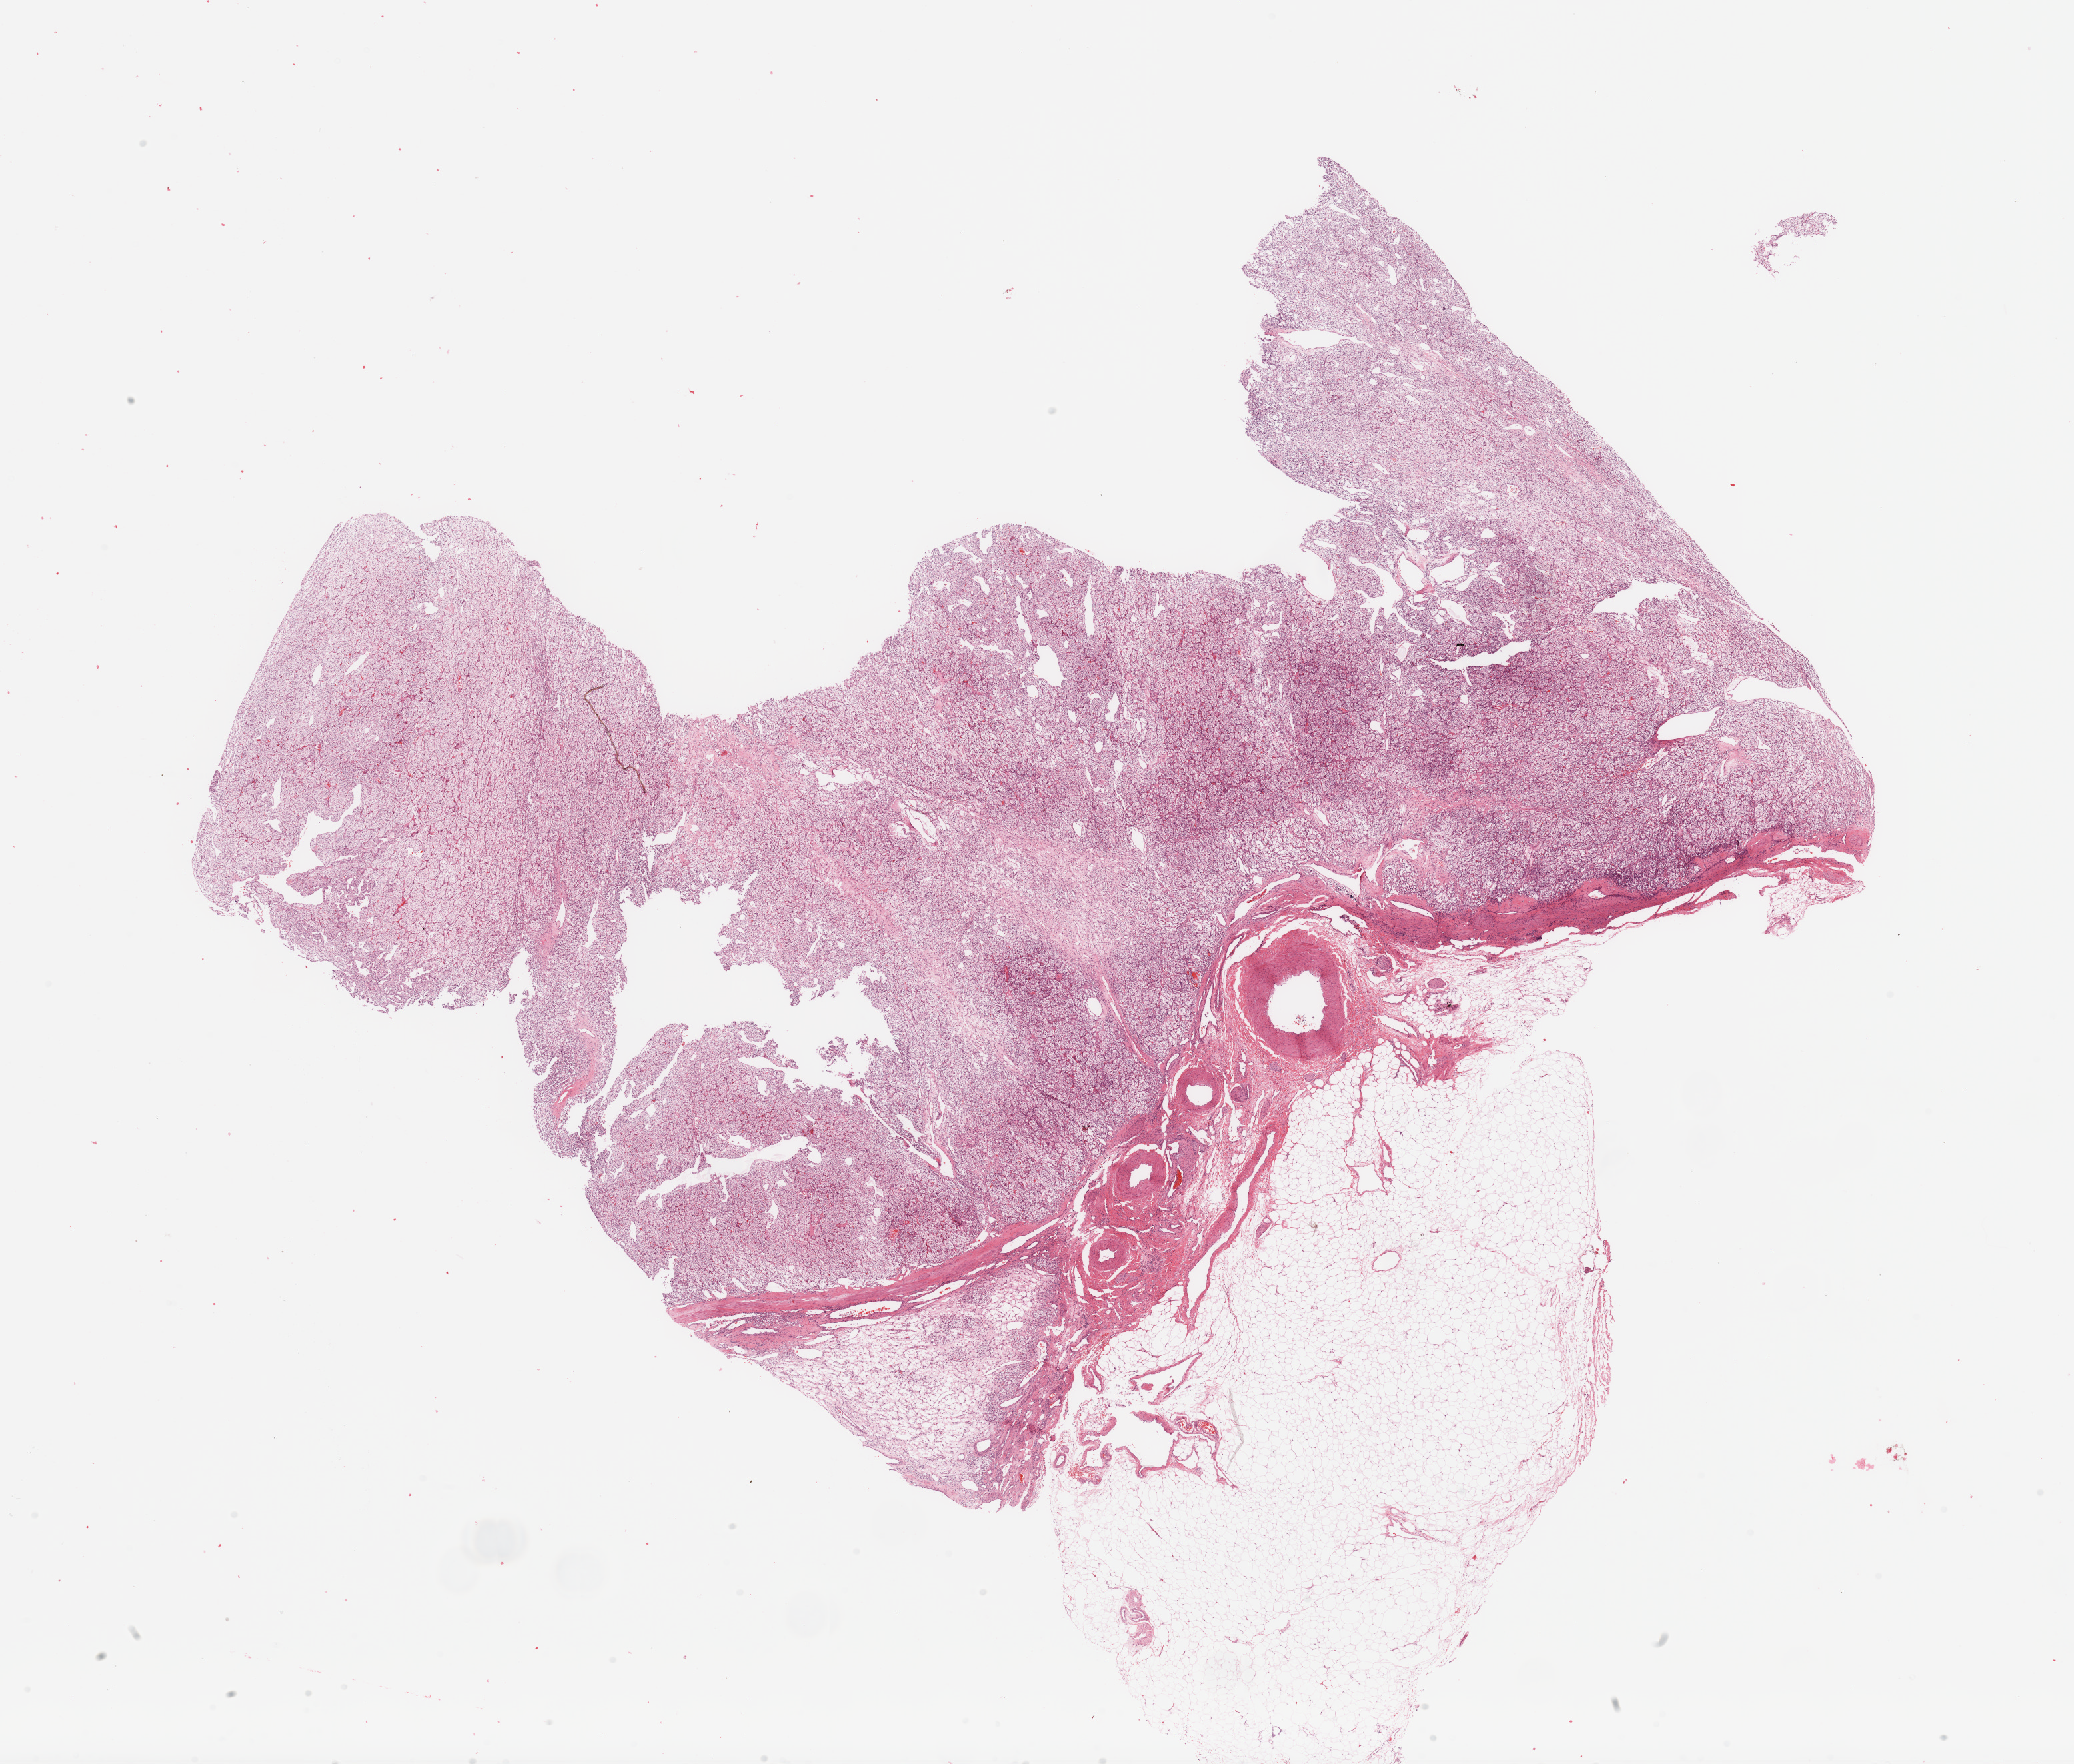
Digitized Hematoxylin and eosin (H&E) stained tissue section (whole slide) — whole scanned area (about 24.6 x 20.9 mm, acquisition: 20x scan) shown as a low-resolution overview, kidney, tumour tissue. Patient: female, age 57 years. Histologic grade: G1 (well differentiated).
Histologic diagnosis: Renal cell carcinoma, NOS.